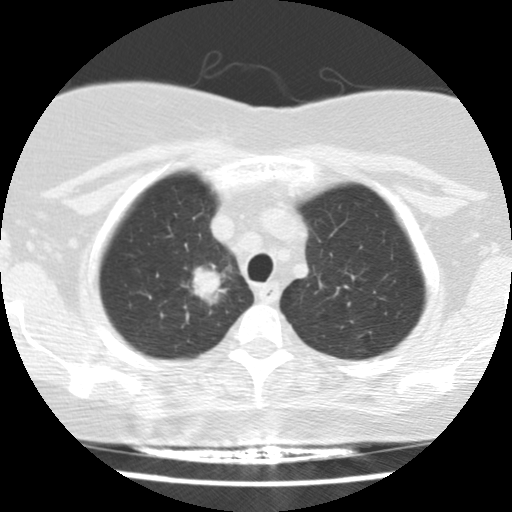
Low-dose screening chest CT, one axial slice; slice 126 of 148 in the series (ordered by position); reconstruction kernel STANDARD; 120 kVp; lung window (W 1500 / L -600 HU); 2.5 mm slice thickness; 512 × 512 image matrix, field of view 281 × 281 mm.
Annotated regions visible in this slice (outlined manually by an expert reader):
- lesion 1 (tumor, upper lobe of right lung): bounding box [x1, y1, x2, y2] px = [192, 265, 226, 305]